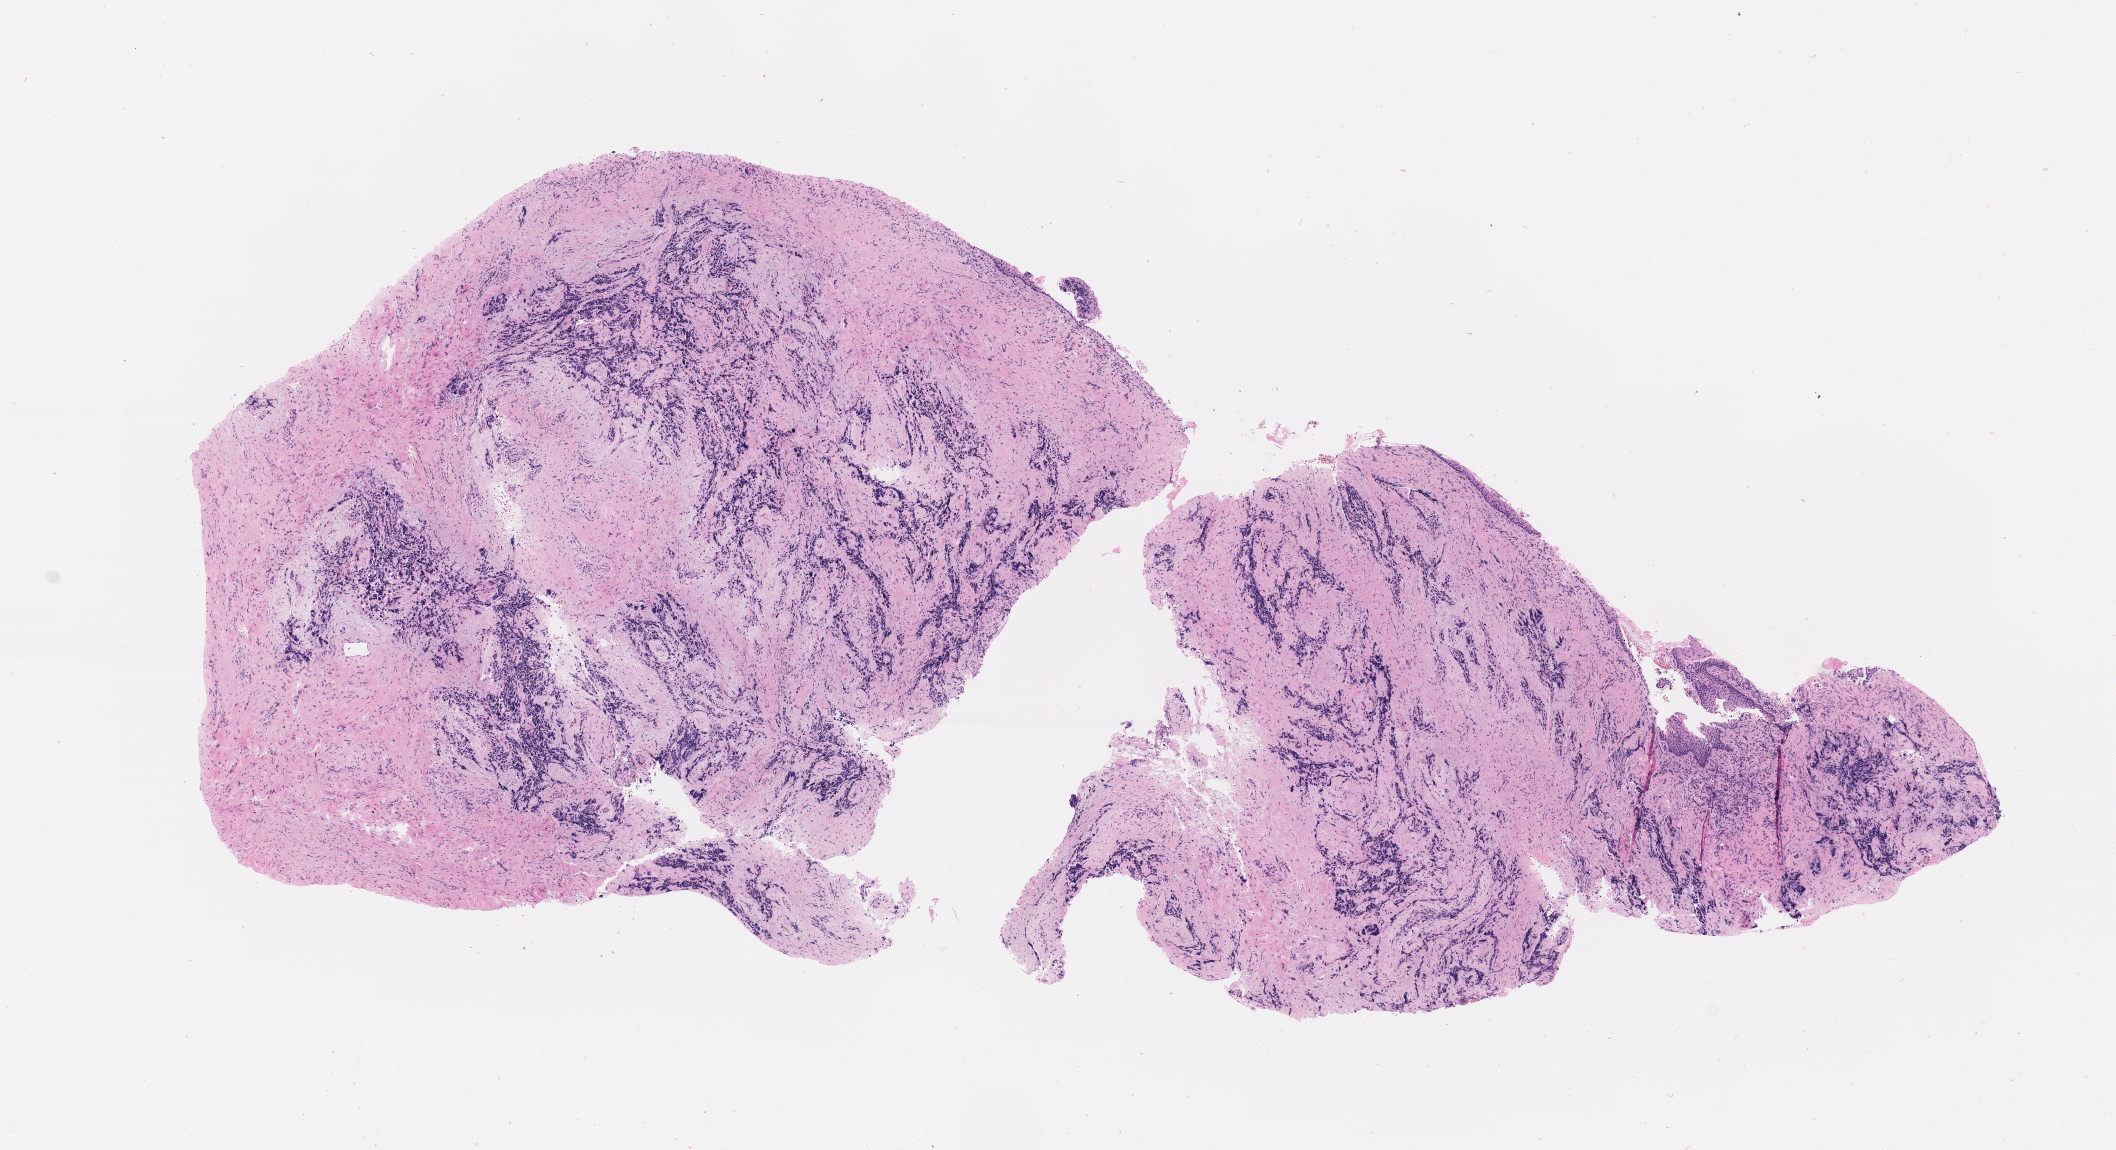
Whole-slide image, haematoxylin and eosin stain, low-resolution overview of the scanned area, about 8.6 x 4.6 mm, specimen: tumor tissue, anatomic site: cervix. Female patient, age 59 years.
* diagnosis: Small cell carcinoma, NOS